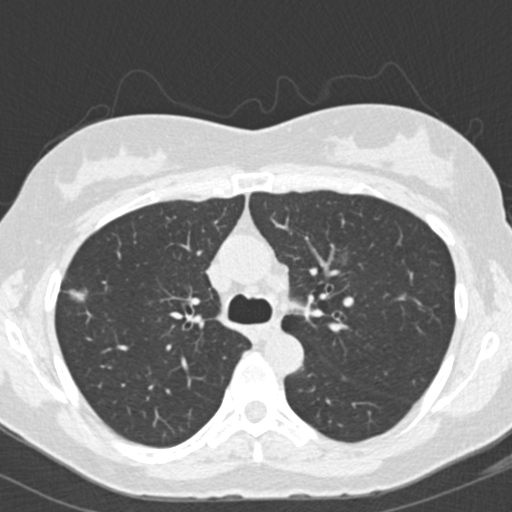
Low-dose screening chest CT, one axial slice; slice 111 of 157 in the series (ordered by position); reconstruction kernel B30f; lung window (W 1500 / L -600 HU); 2 mm slice thickness; 512 × 512 image matrix, field of view 290 × 290 mm.
Outlined on this slice (manually delineated by an expert):
- lesion 1 (tumor, upper lobe of right lung): bounding box [x1, y1, x2, y2] px = [69, 290, 87, 301]